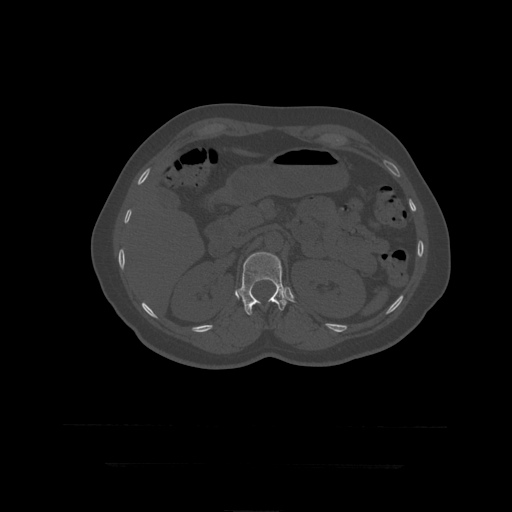
CT including the spine, one axial slice. Position 177 of 399 along the scan axis. Reconstruction kernel STANDARD. 120 kVp. Bone window (W 1800 / L 400 HU). 1.25 mm slice thickness. 512 × 512 image matrix. Patient age 41 years. From the clinical record (not read from this slice): primary cancer: breast.
Outlined on this slice (semi-automatically segmented with operator editing):
- L1 vertebra: bounding box <238,252,288,315> (left, top, right, bottom; pixels)